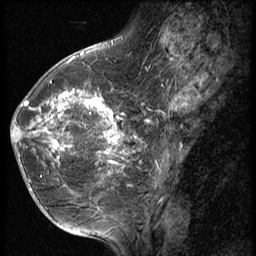
Breast MRI (dynamic contrast-enhanced), one sagittal slice; 3 images stored at this slice position (order not interpretable as contrast timing); 1.5 T; TE 4.2 ms, TR 9 ms; 2.5 mm slice thickness; 256 × 256 image matrix, field of view 180 × 180 mm. Female patient, age 49 years. From the clinical record (not read from this slice): setting: breast cancer imaged before/during neoadjuvant chemotherapy; receptor status: HER2-positive.
Outlined on this slice (semi-automatic segmentation, software-assisted and operator-edited):
- analysis volume of interest (the breast-tissue region the enhancement analysis was run in; not a lesion): bounding box (x1, y1, x2, y2) in pixels: (13, 79, 132, 203)
- tumour enhancement mask (voxels above the 140 % enhancement threshold inside the analysis volume of interest): (13, 90, 130, 173)